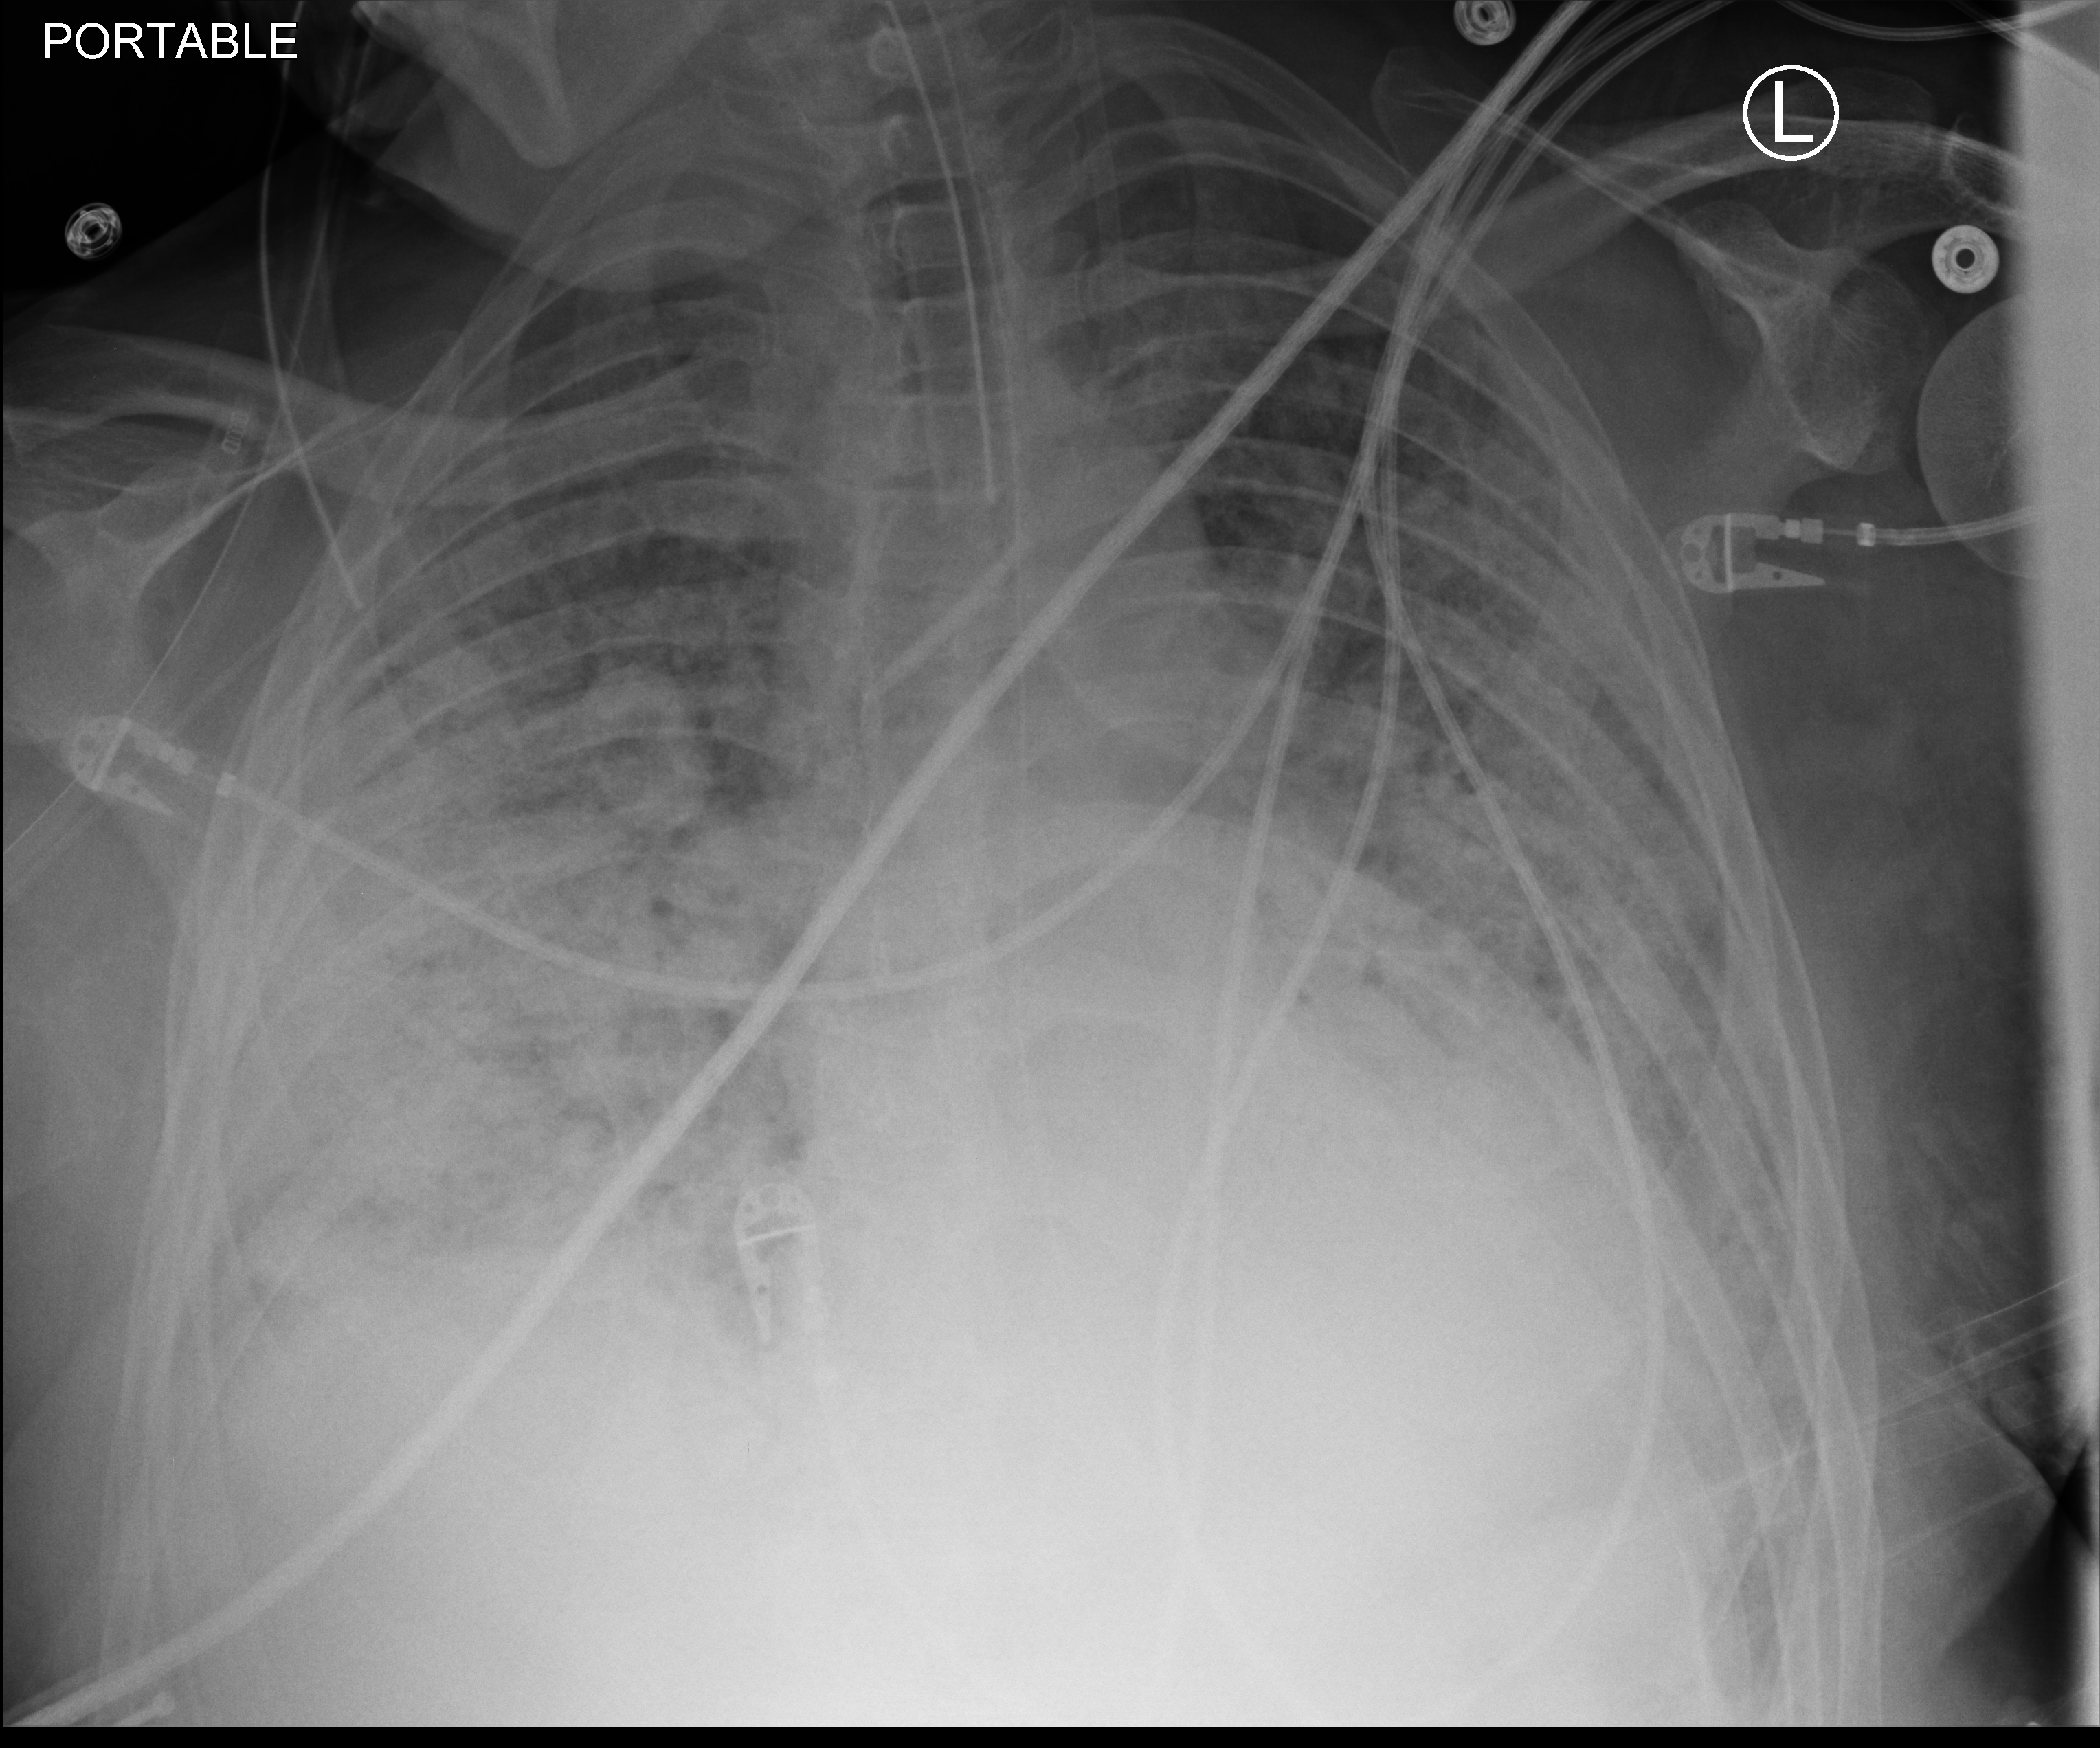
Portable chest radiograph. Male patient hospitalised with COVID-19, age 18–59 years.
Hospital-stay facts (about this admission, not read from this image; timing relative to this image not recorded): diabetes (admission record): no.